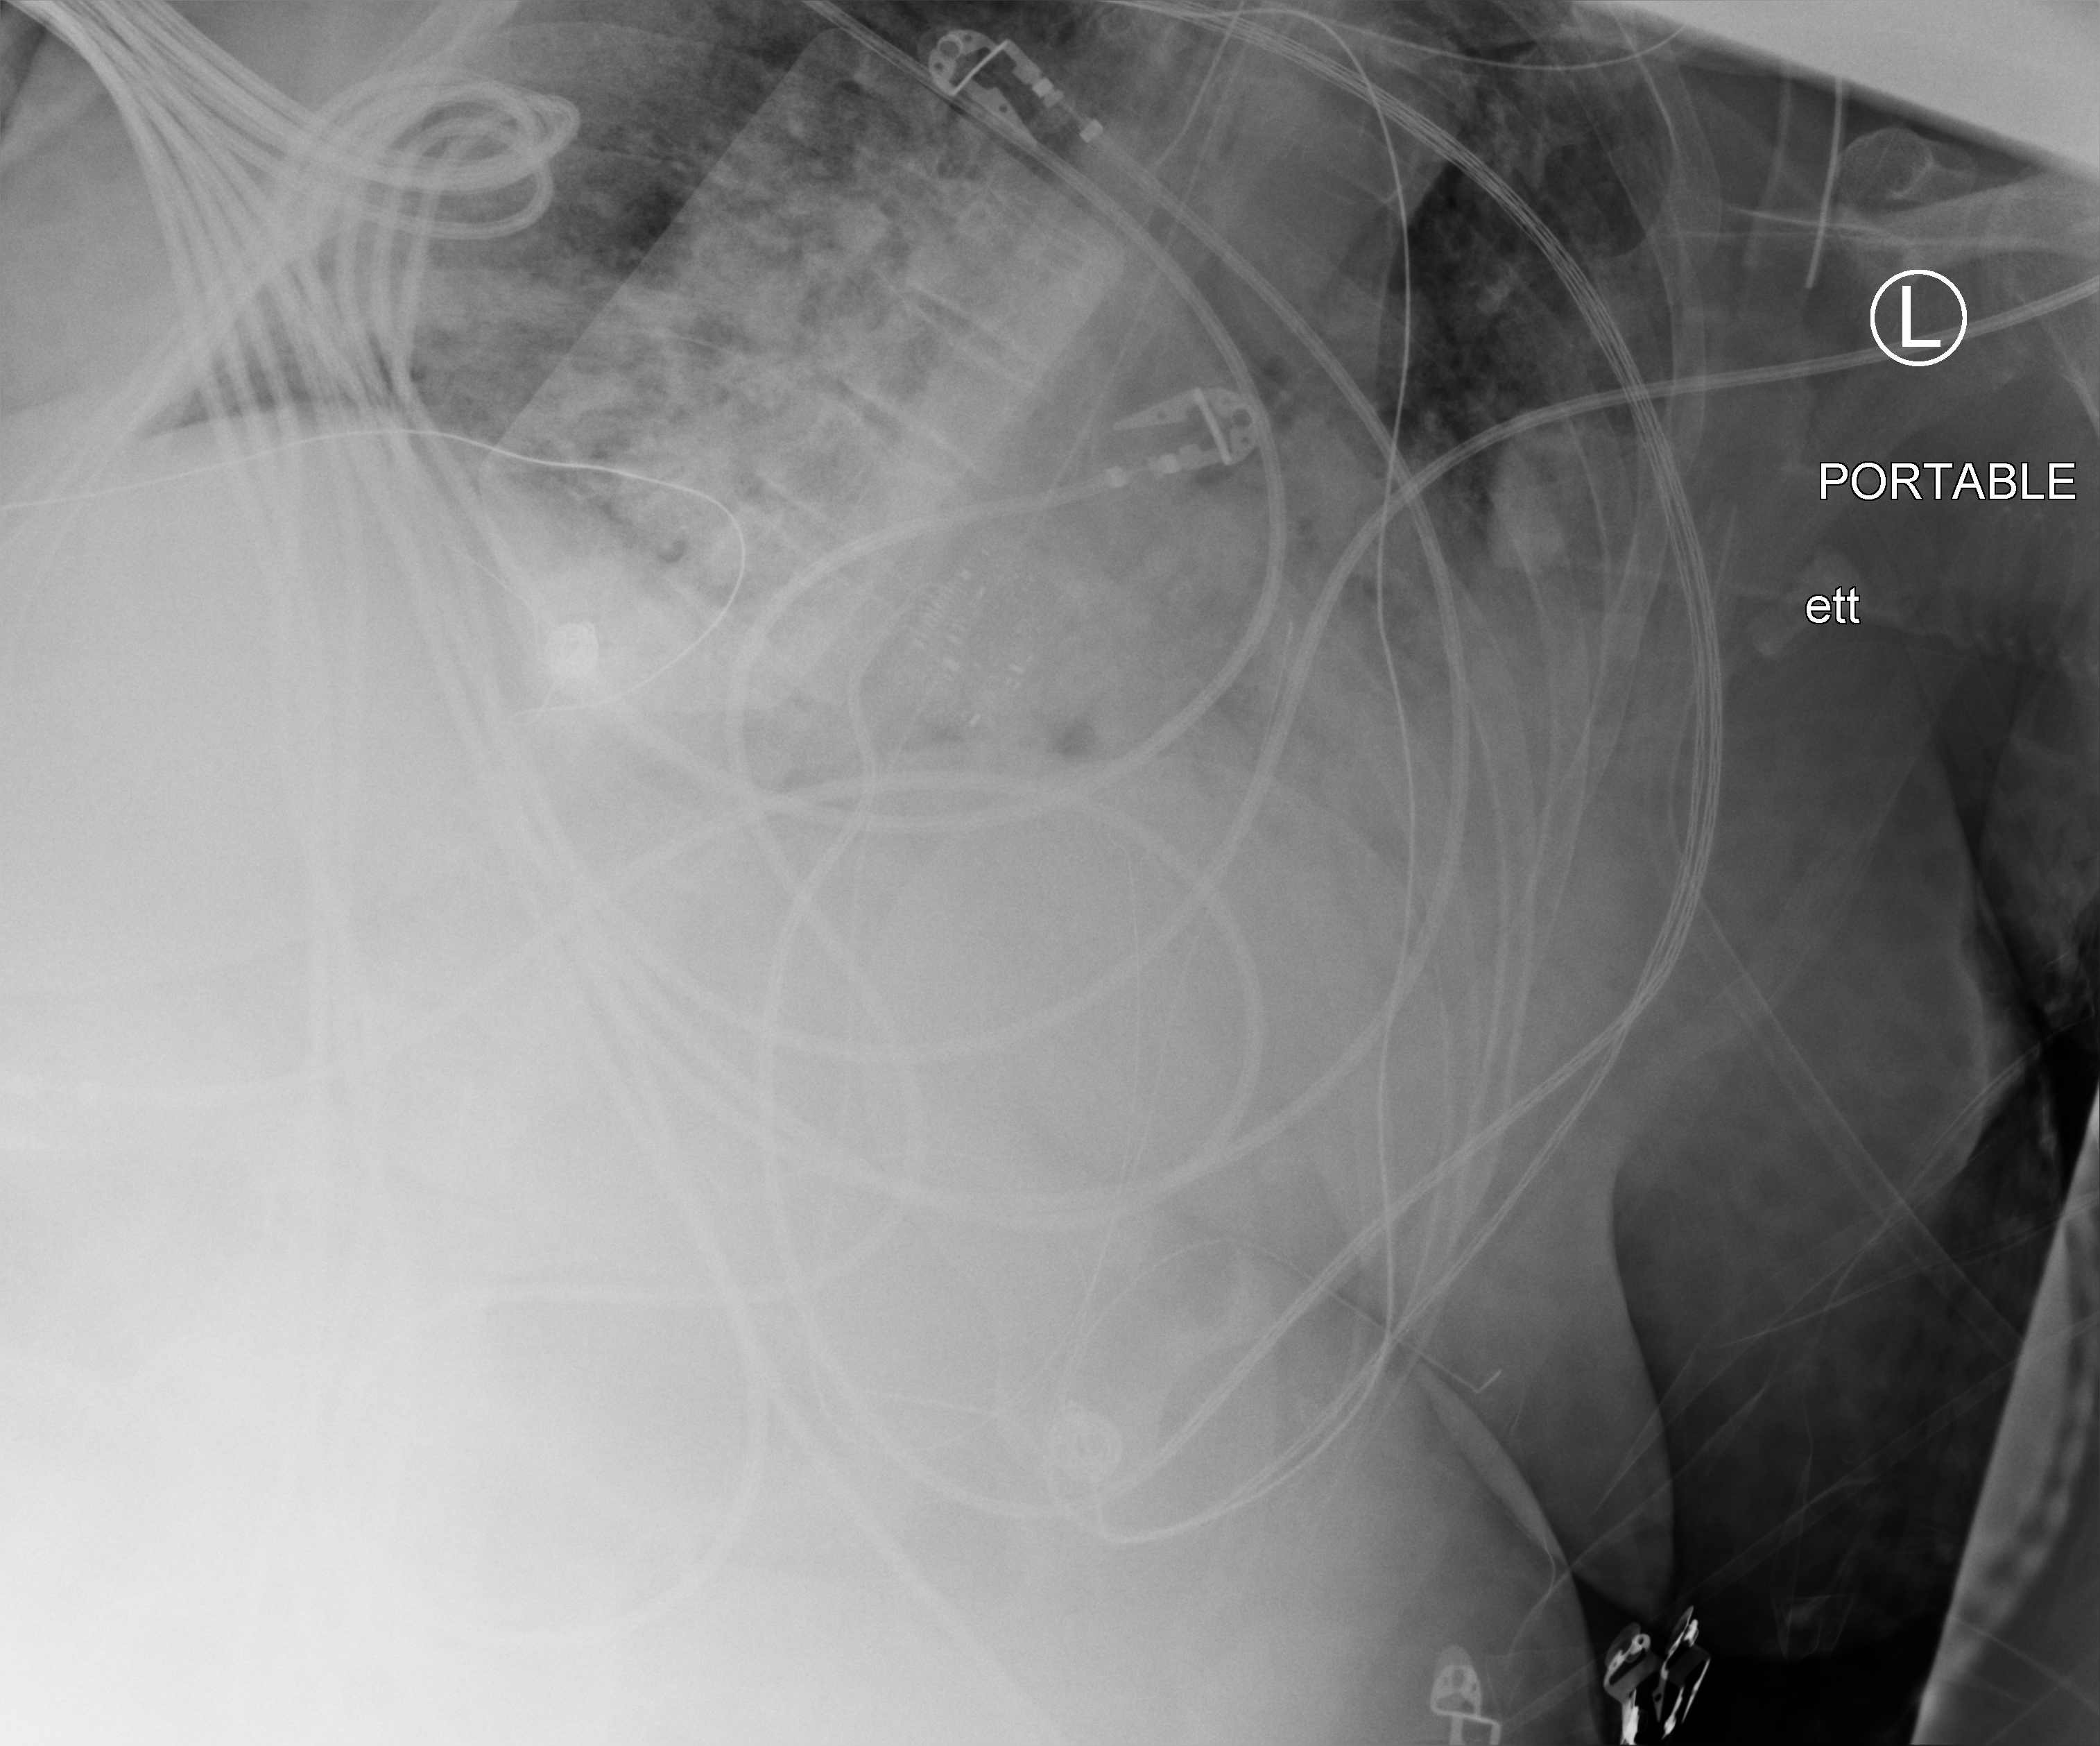
Bedside chest radiograph (computed radiography); anteroposterior (AP) projection. Patient hospitalised with COVID-19; female, aged 60–74 years.
From the hospital-stay record, not from the radiograph (when in the stay this image was taken is not recorded):
- length of hospital stay: 19 days